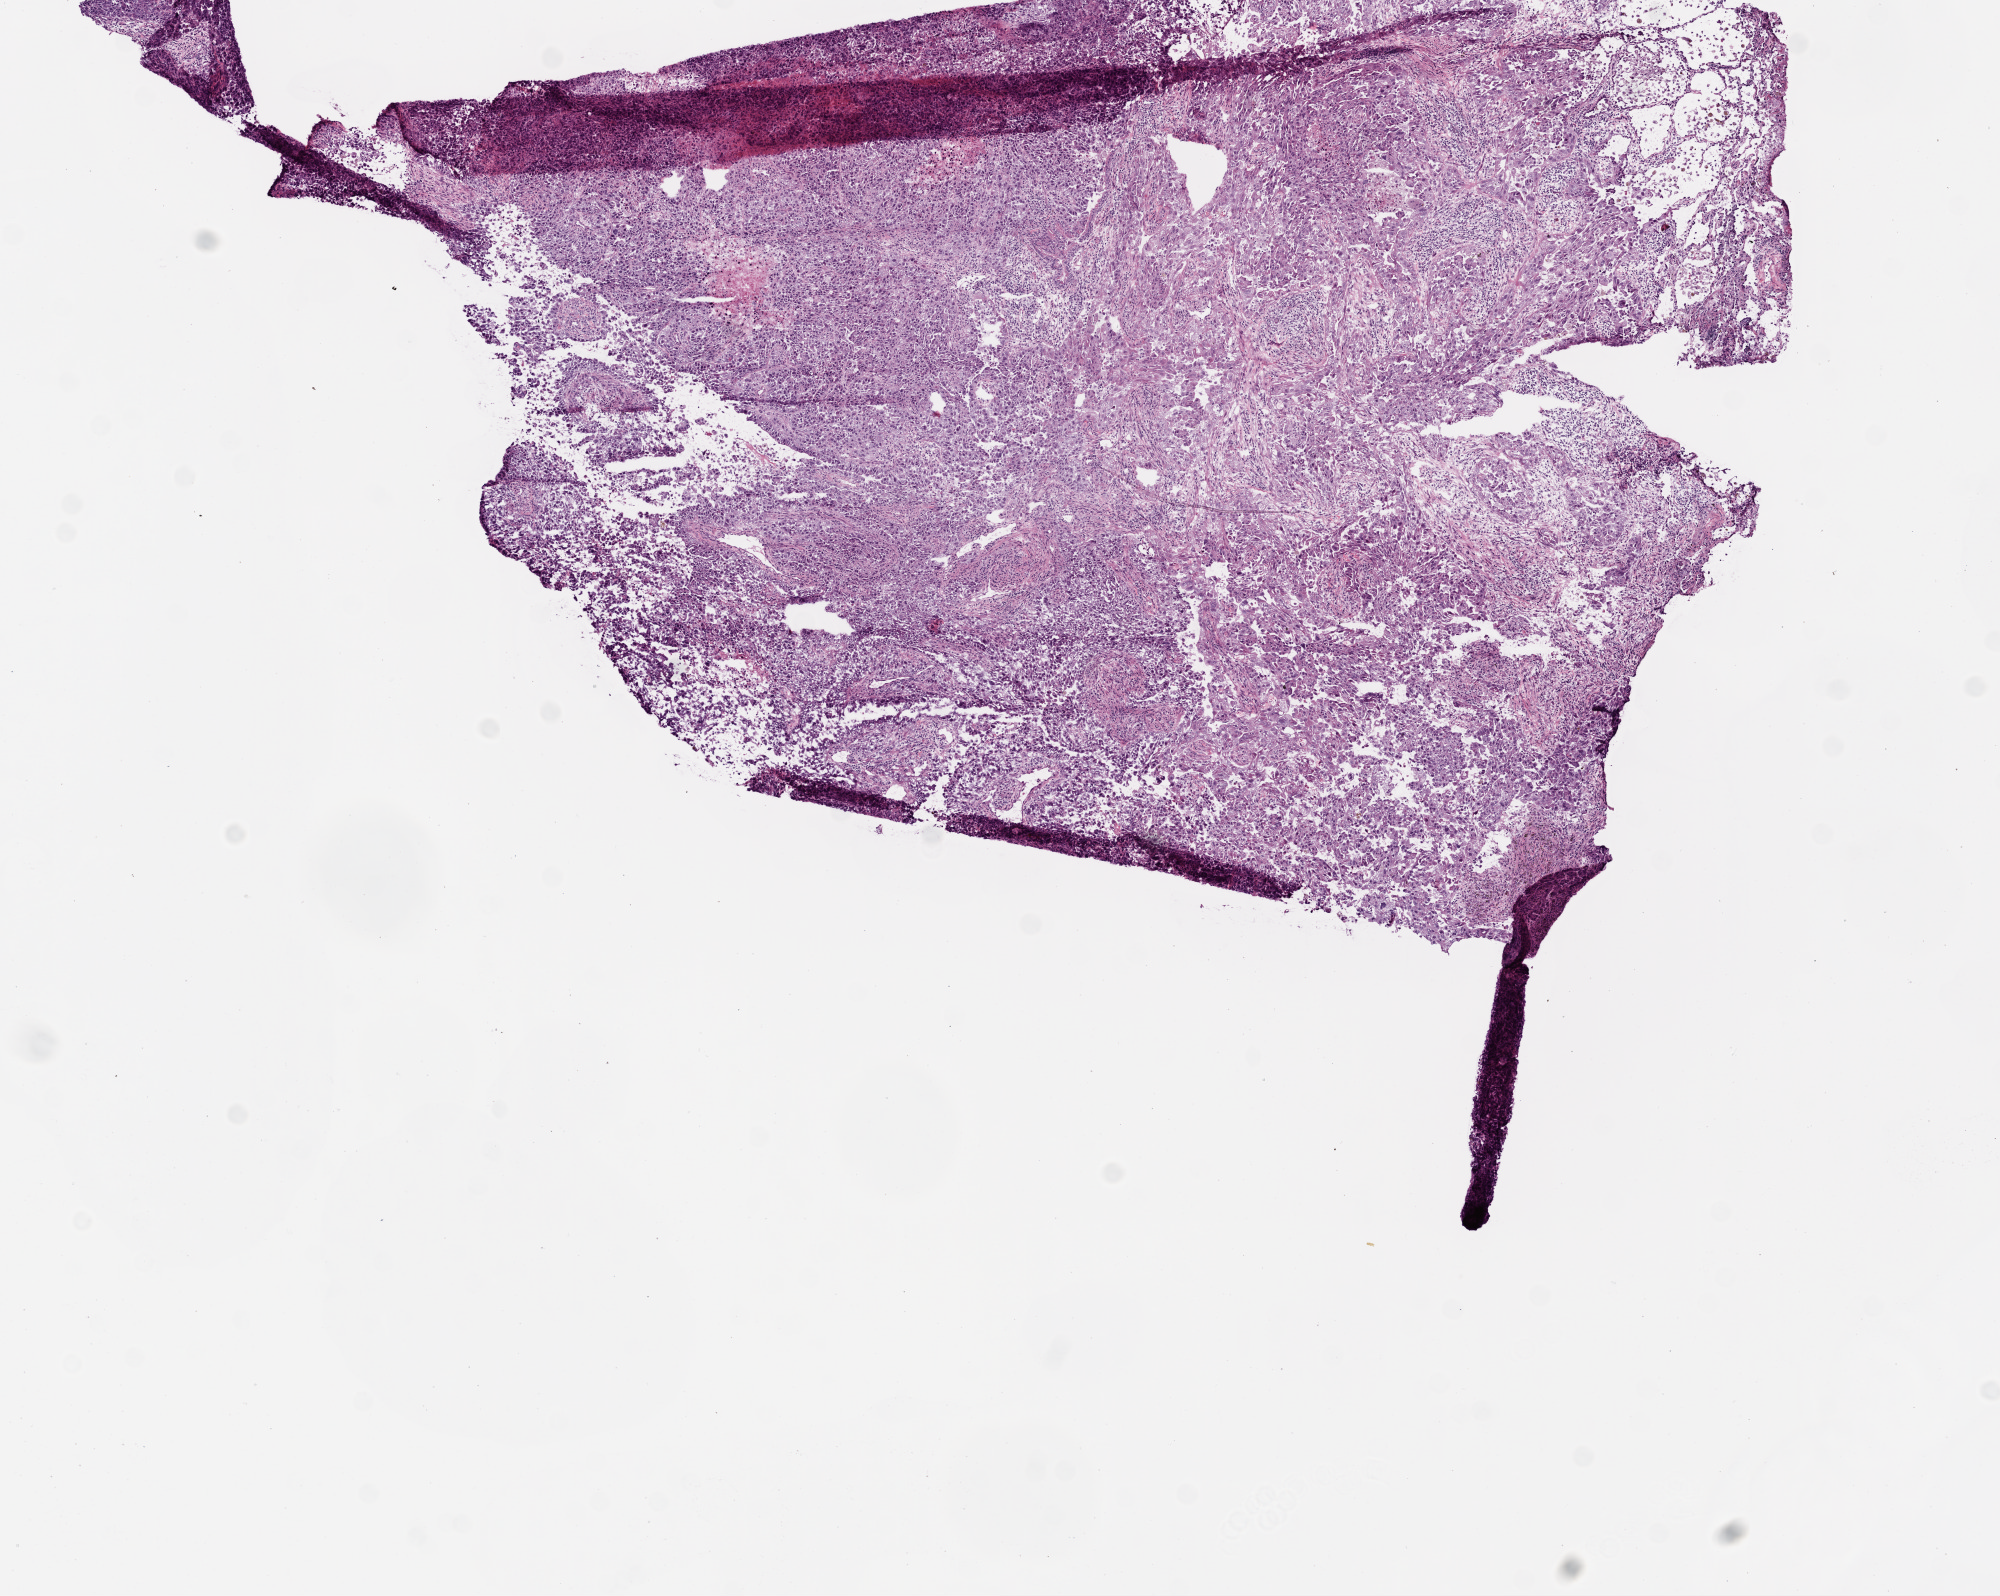
Whole-slide histology image, H&E, a low-resolution overview of the entire scanned area, about 8.0 x 6.4 mm. Frozen section from the top of the tissue portion. Lung, primary tumour sample. Male, age 42 years at initial diagnosis. Composition of this section per pathologist review: tumour cells 88%, tumour nuclei 70%, normal cells 5%, stromal cells 5%, necrosis 2%.
* diagnosis: Adenocarcinoma, NOS (upper lobe, lung)
* AJCC pathologic stage: IV (5th edition)
* laterality: left